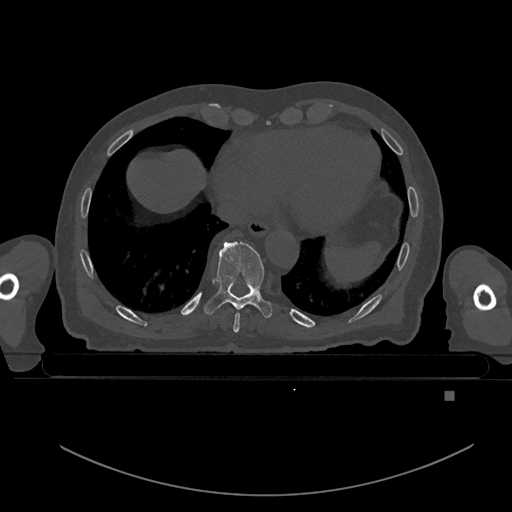
CT including the spine, one axial slice; position 153 of 969 along the scan axis; bone window (W 1800 / L 400 HU); 0.5 mm slice thickness; 512 × 512 image matrix, field of view 456 × 456 mm. Male patient, age 82 years. From the clinical record (not read from this slice): primary cancer: prostate.
Annotated regions visible in this slice (semi-automatically segmented with operator editing):
- T8 vertebra: bounding box <233,312,240,333> (left, top, right, bottom; pixels)
- T9 vertebra: <204,241,272,318>